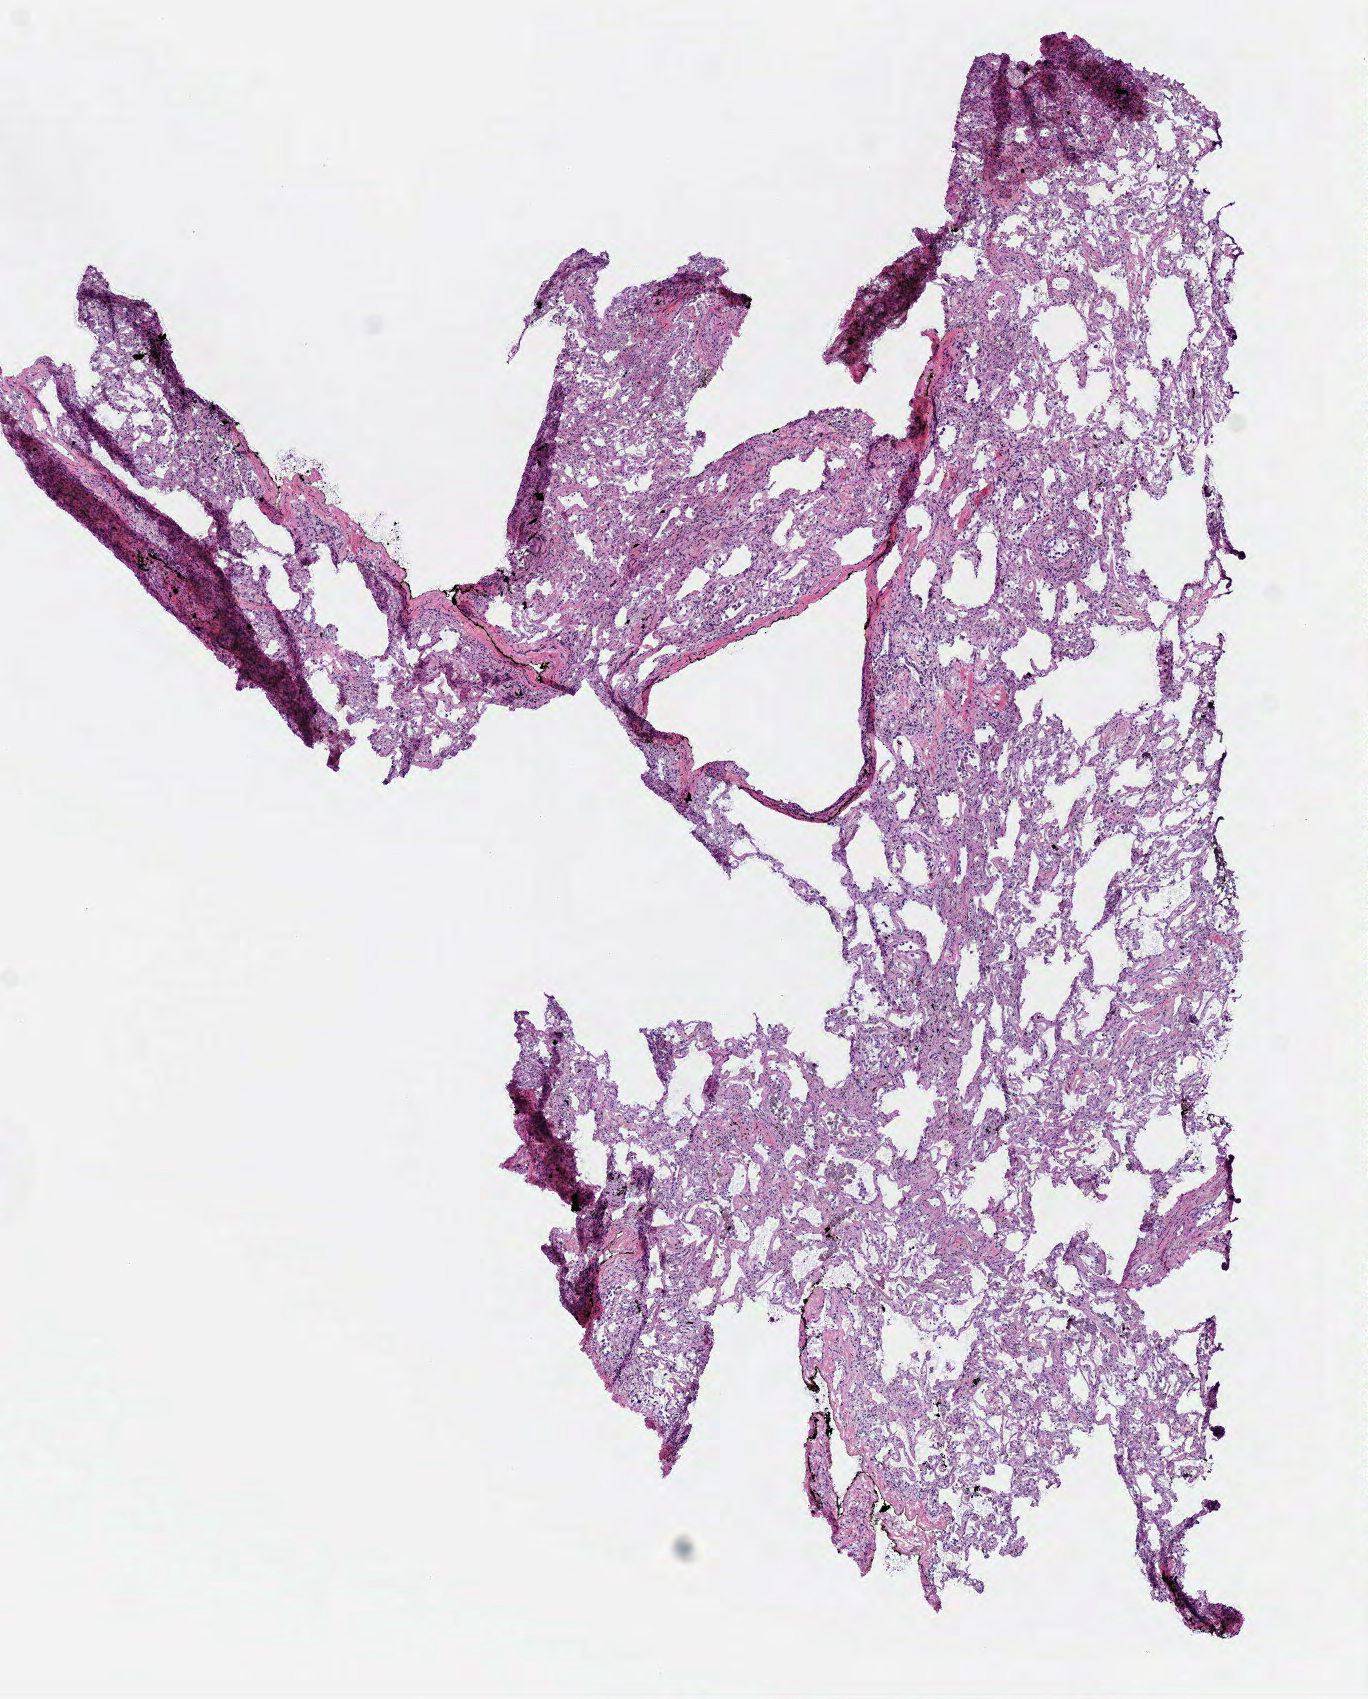
Whole-slide histology image, H&E-stained, low-resolution overview of the scanned area, about 5.4 x 6.7 mm. Frozen section from the bottom of the tissue portion. Lung, primary tumour sample. Patient: male, age at initial diagnosis 64 years. Pathologist review of this section (percent, as recorded): tumour cells 0%, tumour nuclei 0%, normal cells 100%, stromal cells 0%, necrosis 0%.
Pathologic diagnosis: Squamous cell carcinoma, NOS (overlapping lesion of lung). AJCC pathologic stage: IIB.